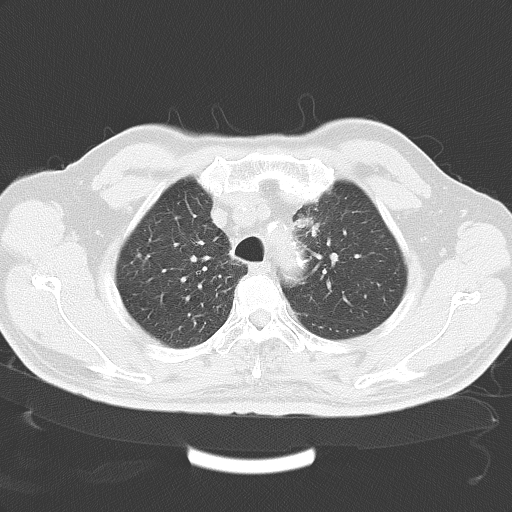
Chest CT, one axial slice. Position 42 of 51 along the scan axis. Reconstruction kernel B70f. 120 kVp. Lung window (W 1500 / L -600 HU). 5 mm slice thickness. 512 × 512 image matrix. Patient: male, 67 years. Case-level facts recorded for this patient, not image findings: clinical TNM (as recorded): T1a N2 M1a.
Annotated regions visible in this slice (bounding box drawn by a radiologist):
- lung tumour (recorded histology: large cell carcinoma): box from (x=289, y=215) to (x=322, y=236) px